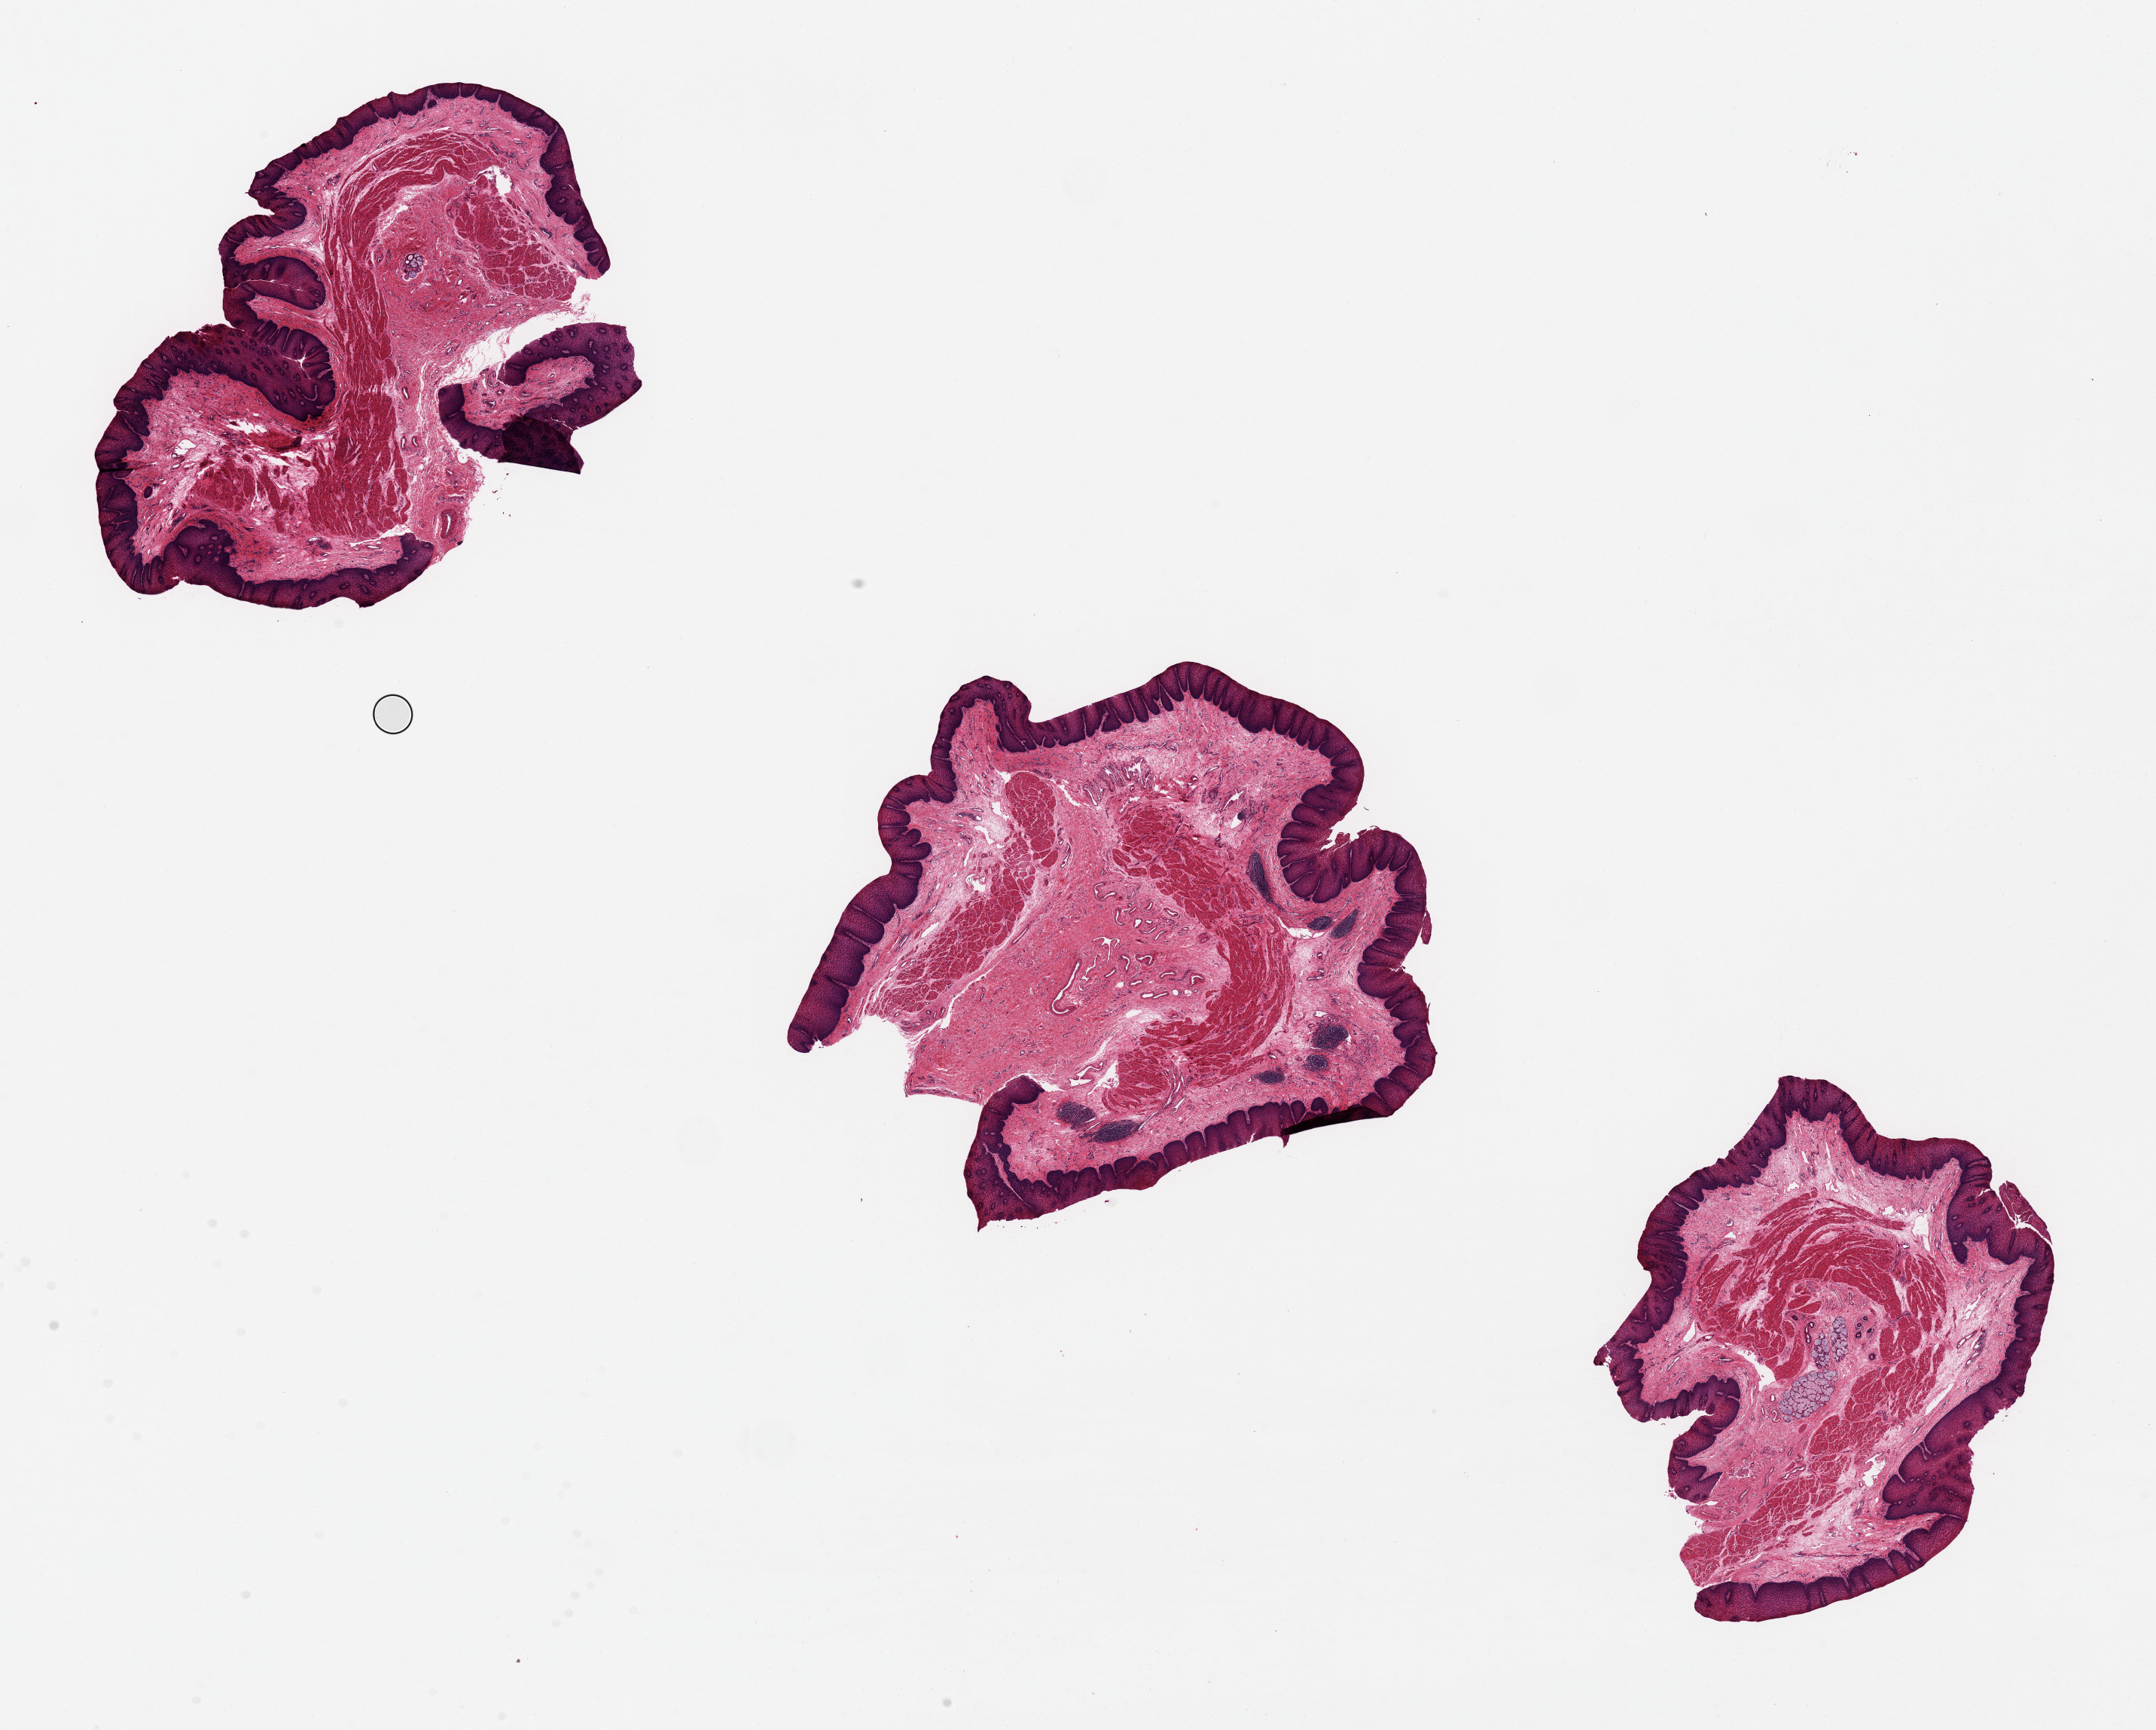
Whole-slide image, hematoxylin and eosin (H&E) stain, brightfield — shown as a low-resolution overview of the whole scanned area (about 22.6 x 18.2 mm, acquisition: 20x scan); PAXgene-fixed, paraffin-embedded tissue; sampled site (target tissue): esophageal mucous membrane; donor tissue sample. Donor: male.
Review note (as recorded): 0-1. Epithelial thickness ranges from 245-445microns.